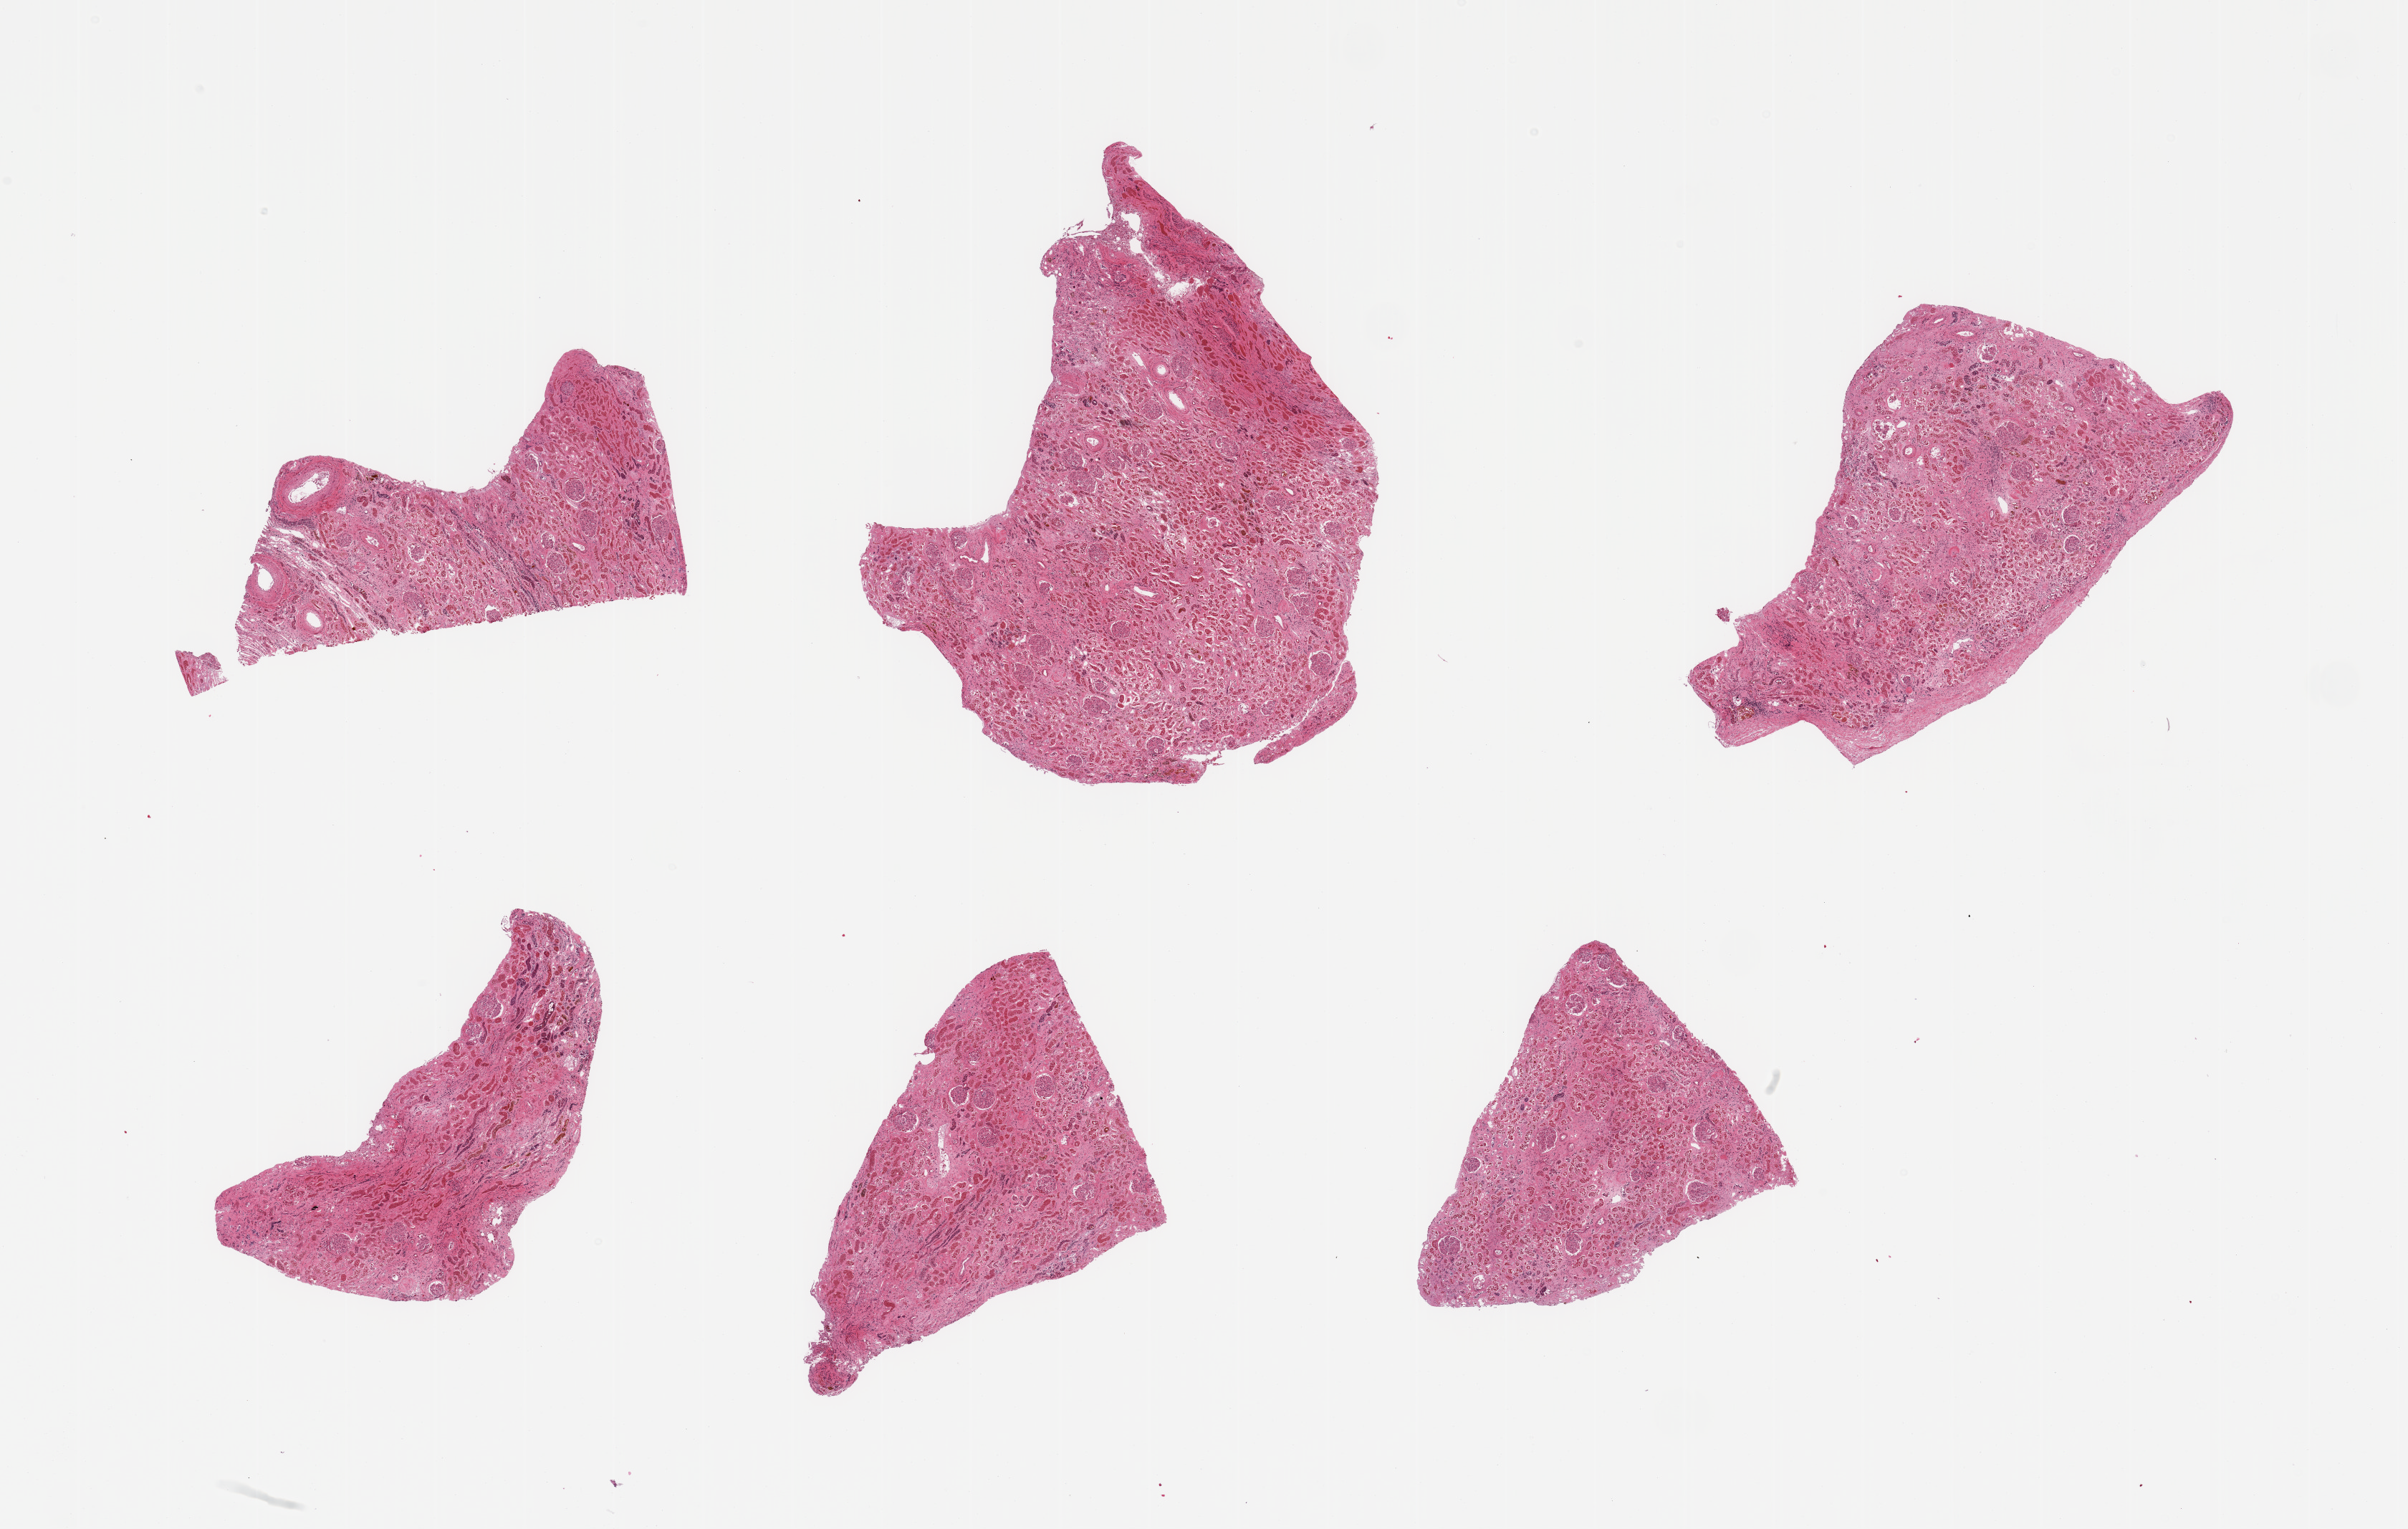
Haematoxylin and eosin whole-slide image, whole scanned area (about 26.6 x 16.9 mm) shown as a low-resolution overview; PAXgene-fixed, paraffin-embedded tissue; target tissue: renal cortex; tissue donor sample. Male donor.
Reviewer comment on this tissue sample: 6 pieces; glomeruli present; advanced autolysis.